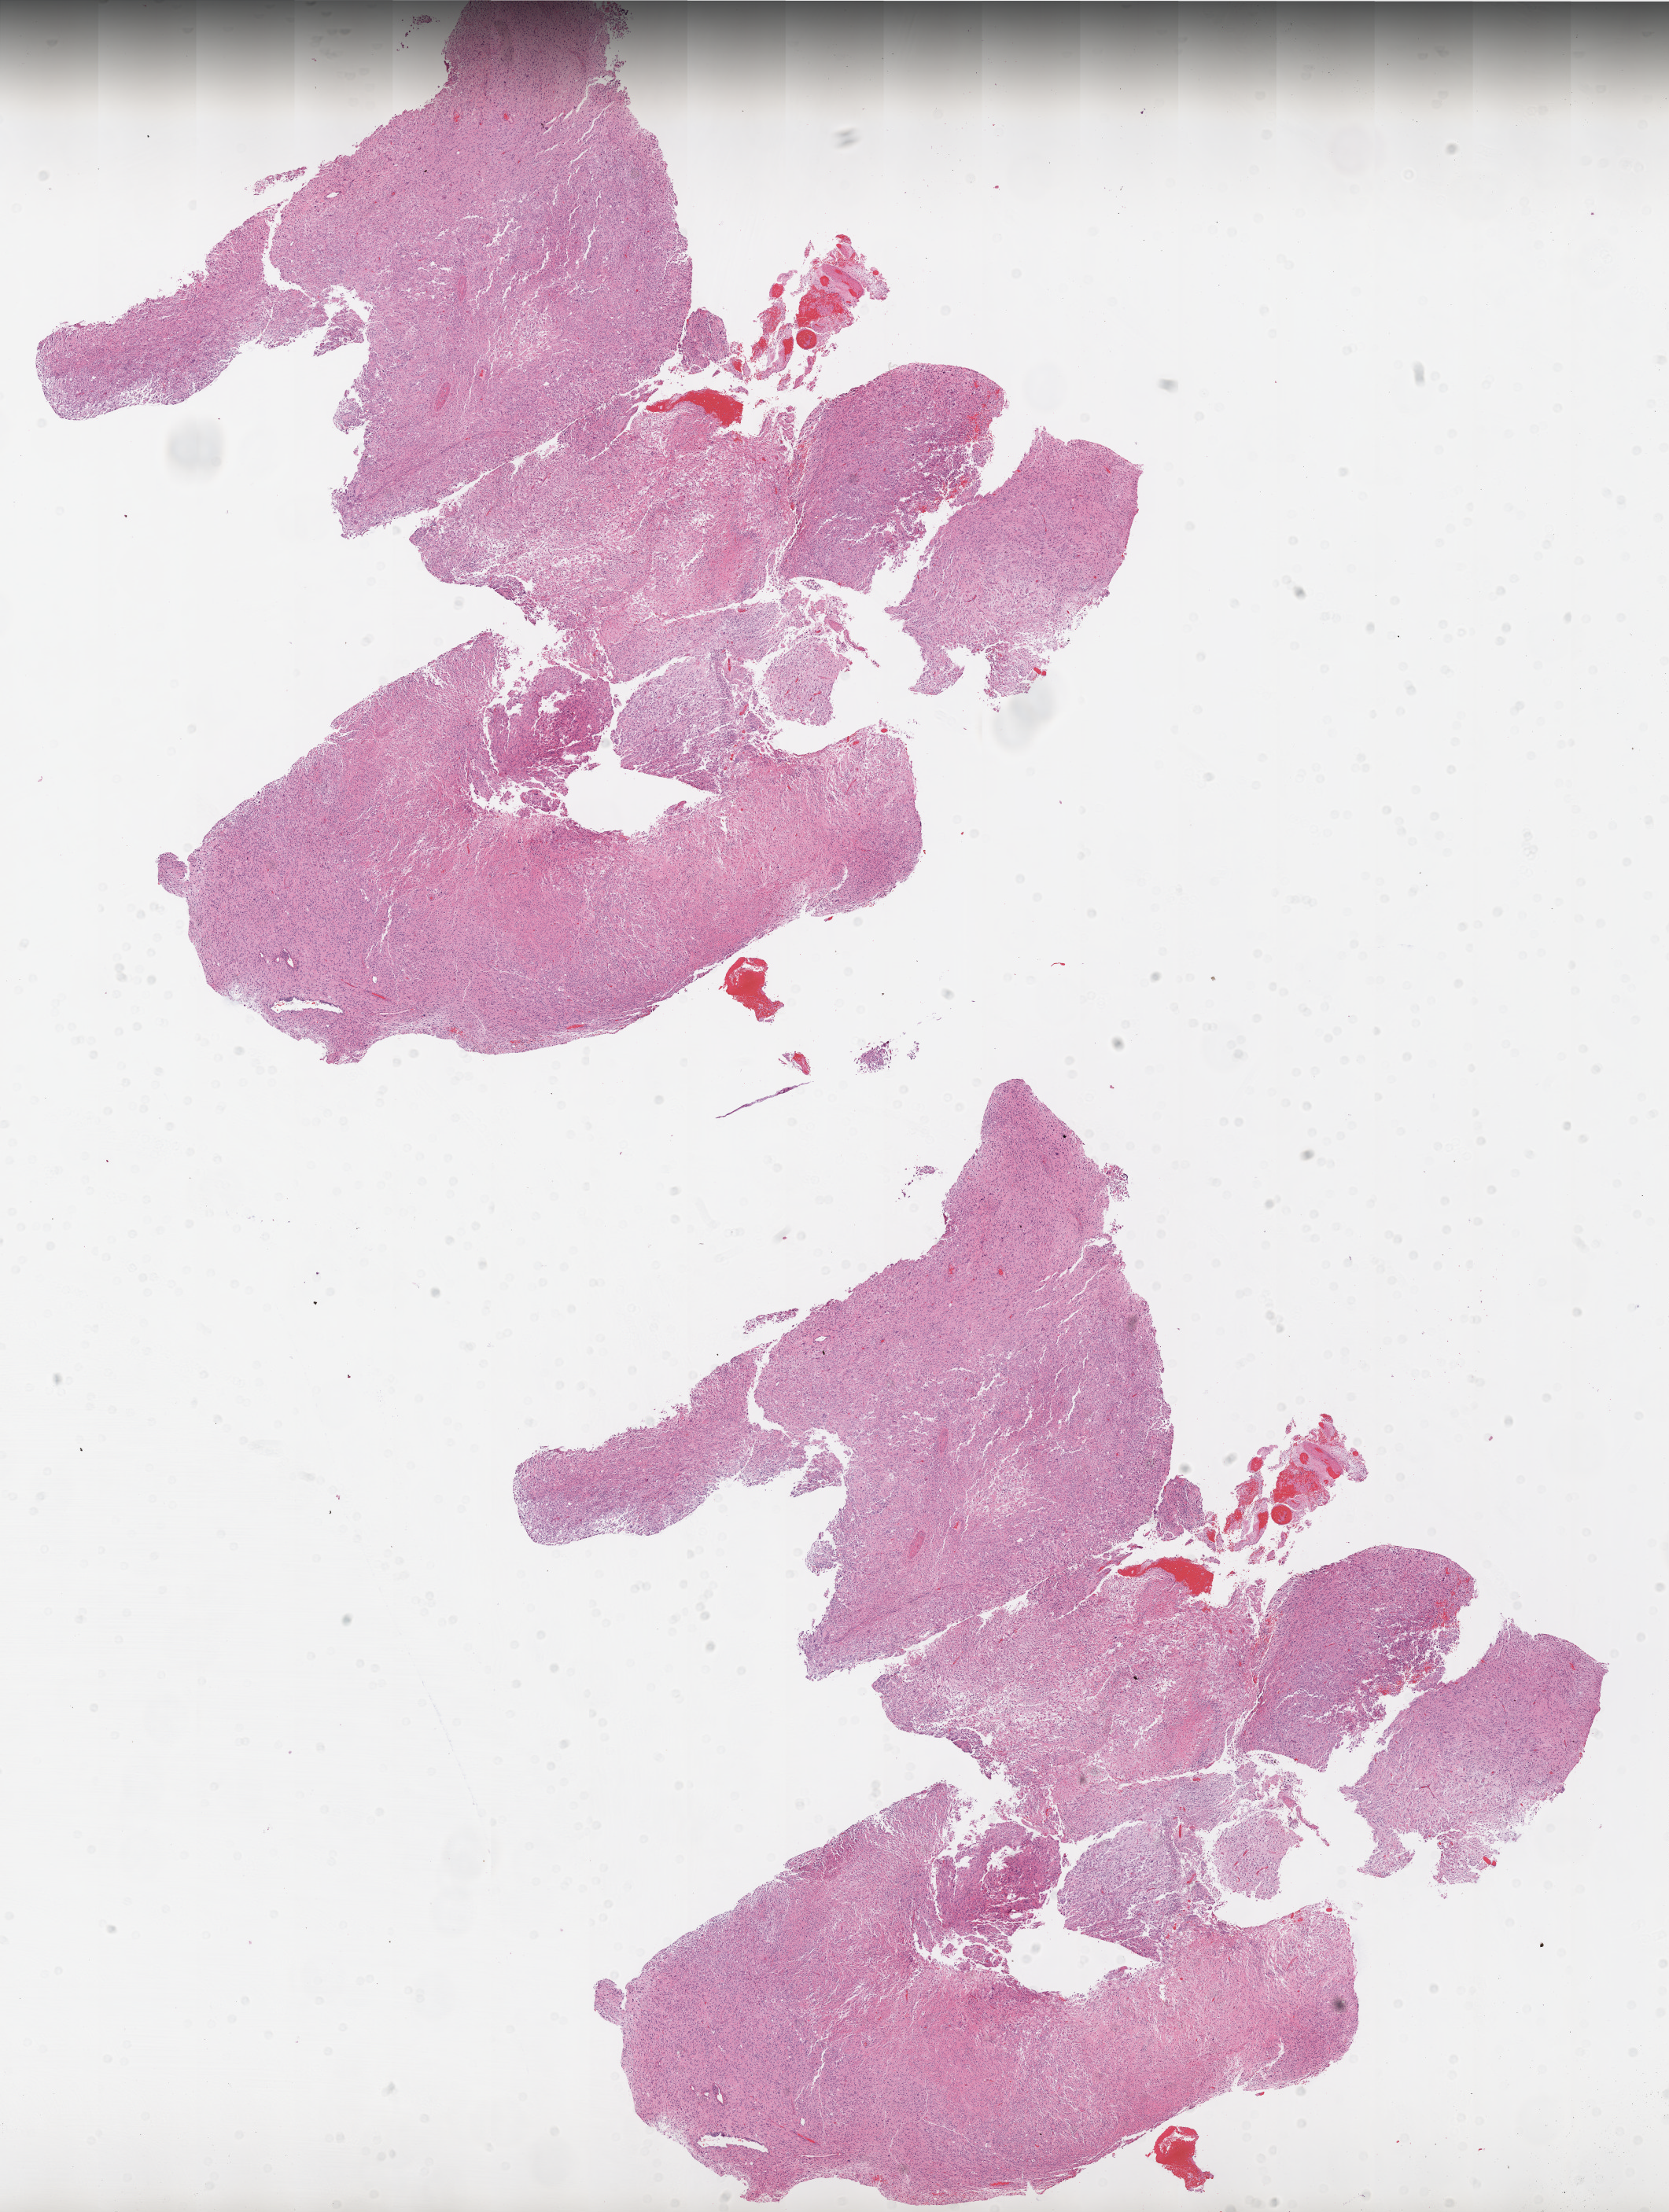
Digitized H&E tissue section (whole slide) — whole scanned area (about 17.0 x 22.5 mm, slide scanned at 20x) shown as a low-resolution overview. Formalin-fixed paraffin-embedded (FFPE) diagnostic section. Primary tumour sample from the brain. Female, age 65 years at initial diagnosis.
Pathologic diagnosis: Glioblastoma.